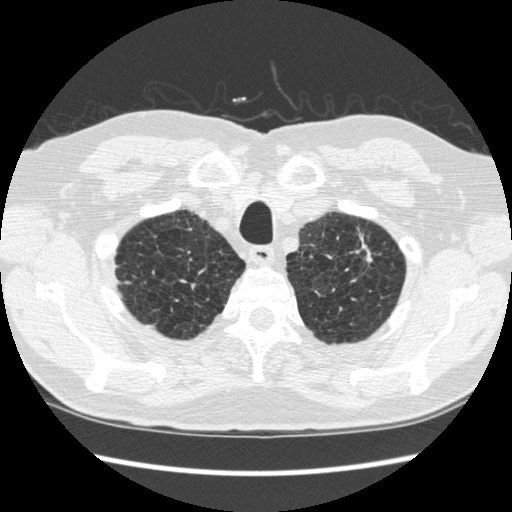
Chest CT (low-dose screening protocol), one axial image, second screening round (one year after baseline), lung window (W 1500 / L -600 HU), 1.25 mm slice thickness, 120 kVp, slice 40 of 295 in the series. Male, age 70 years at enrolment.
Expert reader's lesion annotation, bounding box (x1, y1, x2, y2) in pixels: (328, 225, 390, 293). The screening reader recorded 5 non-calcified nodules or masses ≥4 mm on this exam (right lower lobe, right lower lobe, right lower lobe, left upper lobe, left lower lobe); which of them this box marks is not recorded.